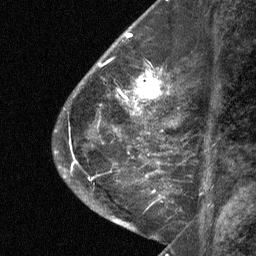
Breast MRI (dynamic contrast-enhanced), one sagittal slice. Slice 23 of 64 in the series (ordered by position). Dynamic contrast-enhanced study with each time point stored as its own series, time point 2 of 3 at this slice position (early post-contrast, ordered by acquisition time). 1.5 T. TE 4.8 ms, TR 27 ms. 256 × 256 image matrix. Patient: female, 59 years. From the clinical record (not read from this slice): setting: breast cancer imaged before/during neoadjuvant chemotherapy; receptor status: triple-negative.
Annotated regions visible in this slice (semi-automatically segmented with operator editing):
- analysis volume of interest (the breast-tissue region the enhancement analysis was run in; not a lesion): bounding box <122,60,176,109> (left, top, right, bottom; pixels)
- tumour enhancement mask (voxels above the 90 % enhancement threshold inside the analysis volume of interest): <132,69,163,109>